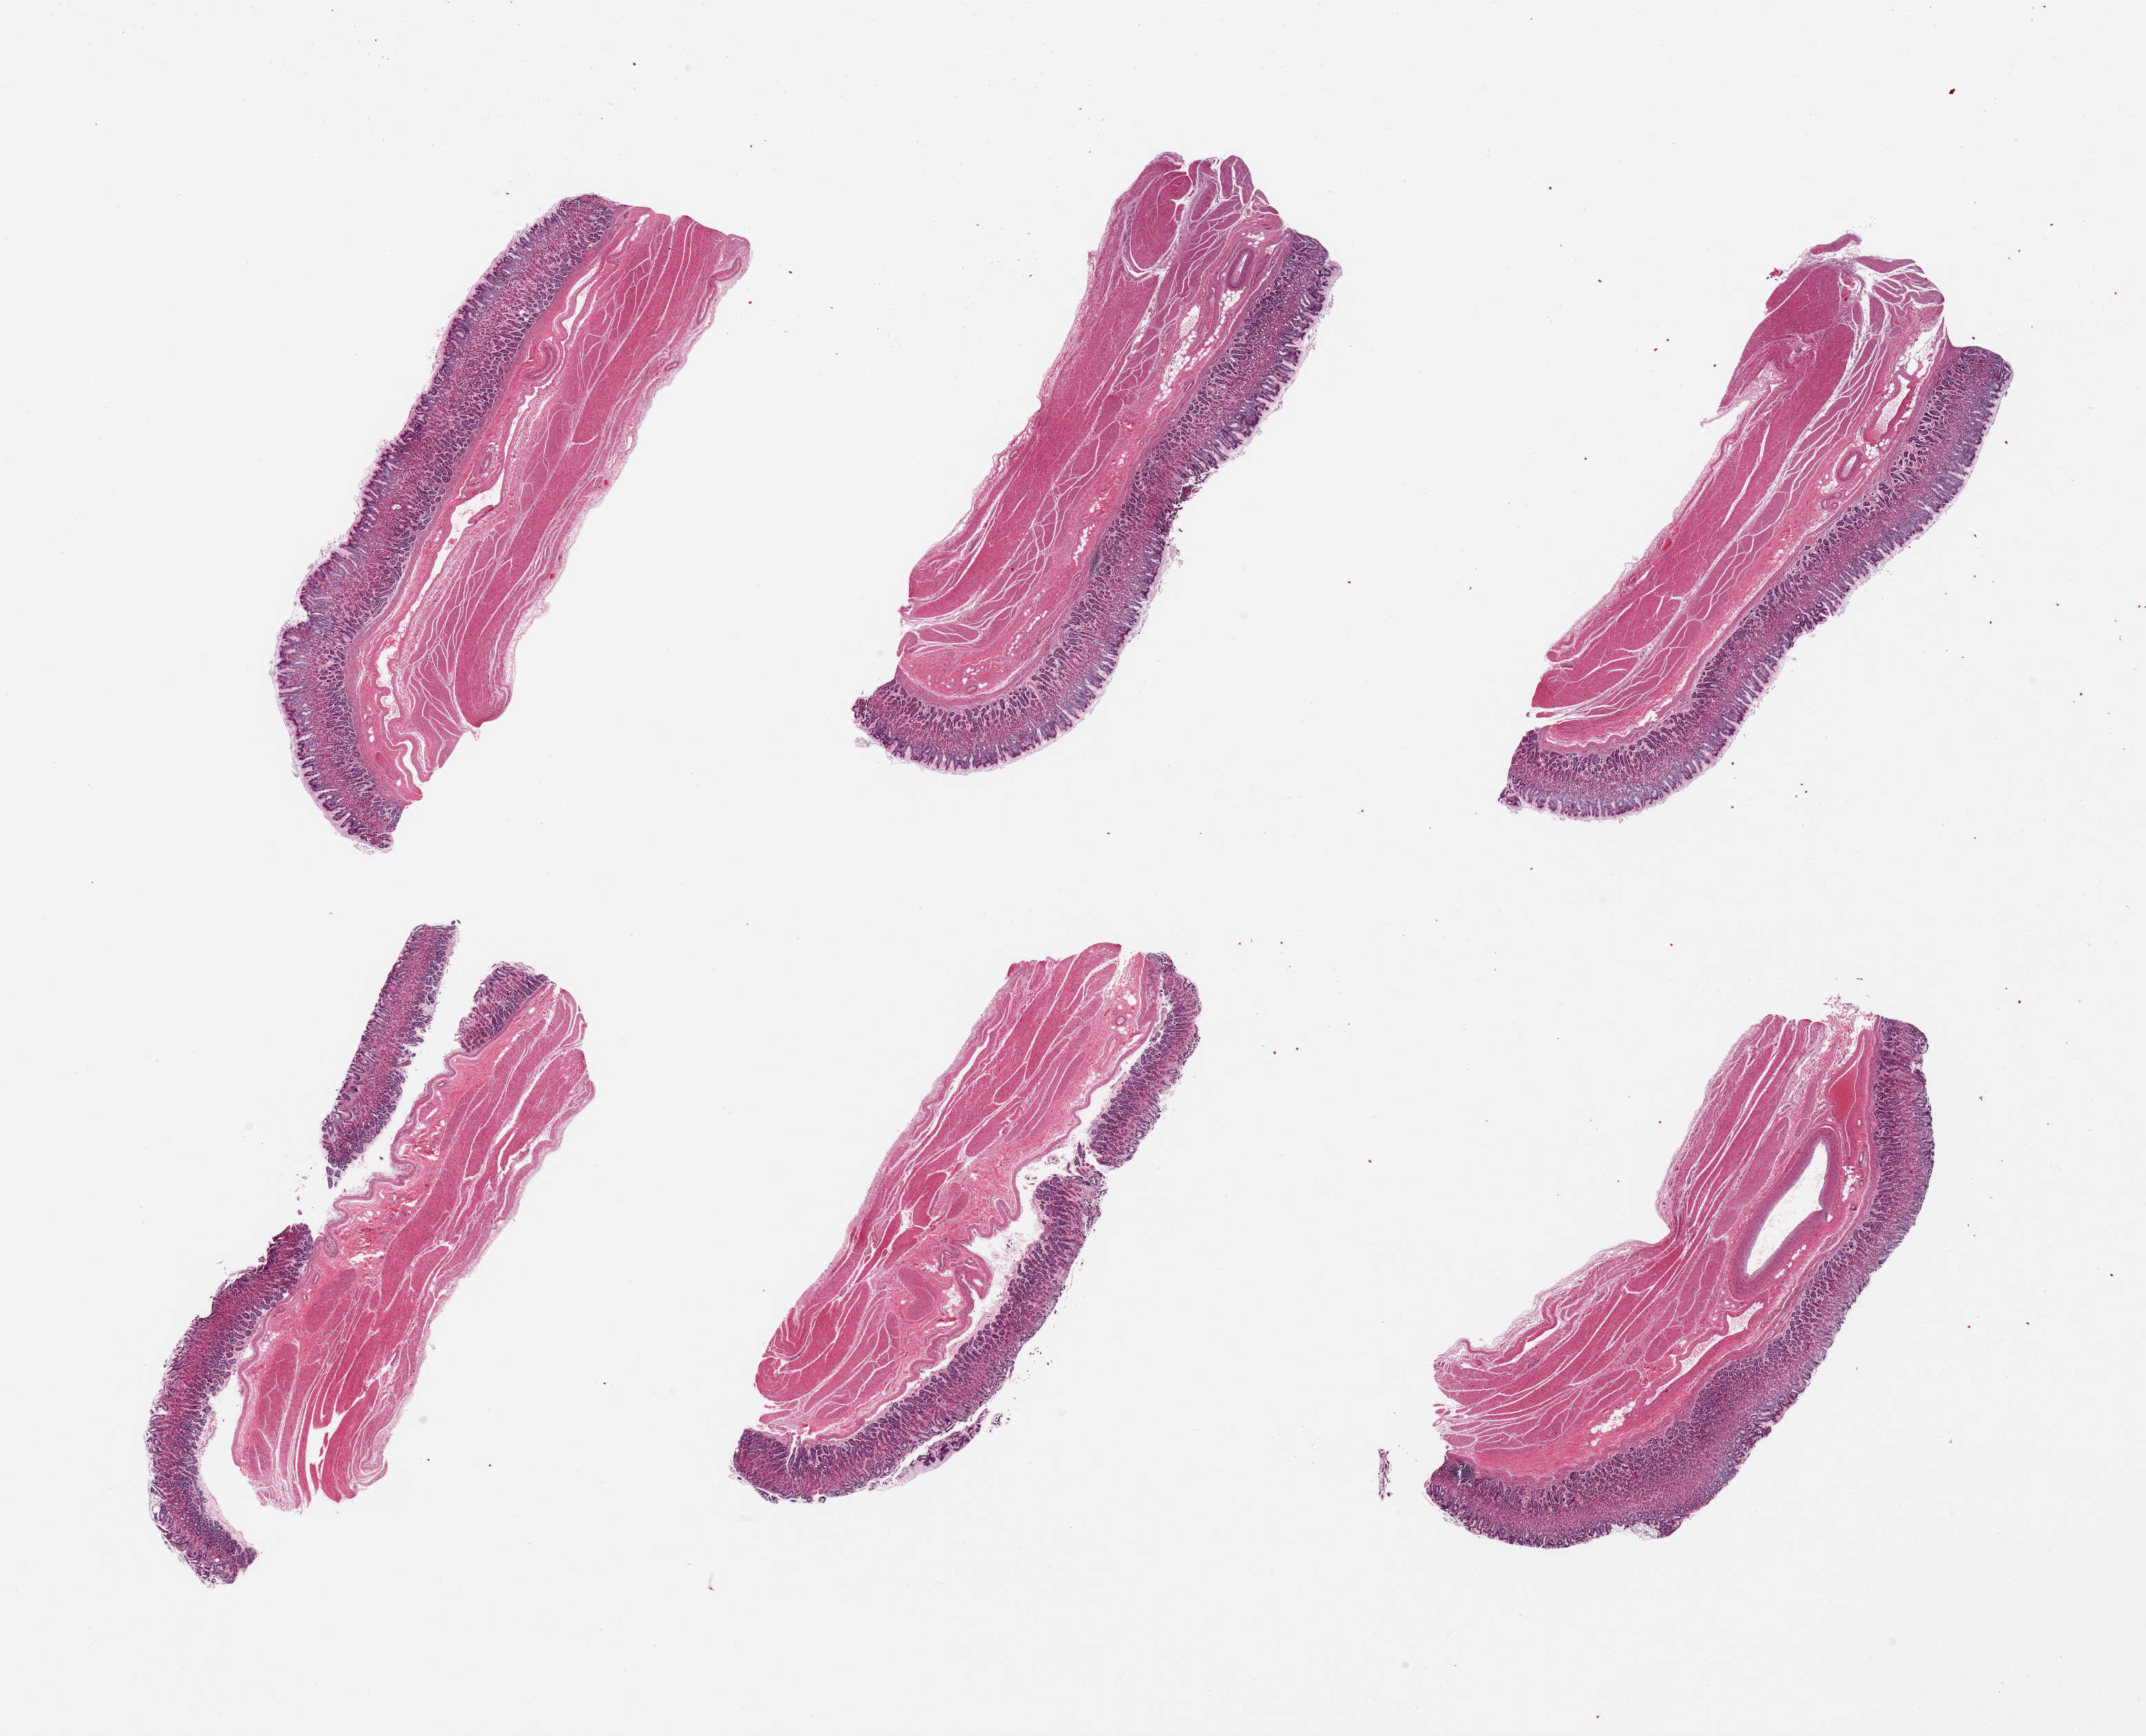
Whole-slide image, H&E stain — shown as a low-resolution overview of the whole scanned area (about 24.6 x 19.9 mm). PAXgene-fixed, paraffin-embedded tissue. Section of stomach (target tissue). Tissue donor sample. Donor sex: male.
Review note (as recorded): 6 pieces; mild to moderate autolysis; gastric mucosa and muscularis.